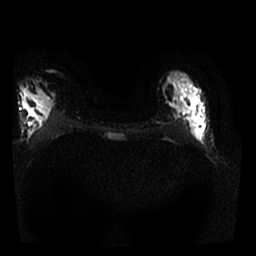
Breast MRI, one axial slice; slice 12 of 25 in the series (ordered by position); diffusion-weighted series; image 2 of 4 stored at this slice position (different b-values; order by instance number); 1.5 T; 256 × 256 image matrix. Female patient.
Structures marked on this image (manually delineated by an expert):
- tumour on diffusion-weighted imaging: bounding box <195,118,205,146> (left, top, right, bottom; pixels)